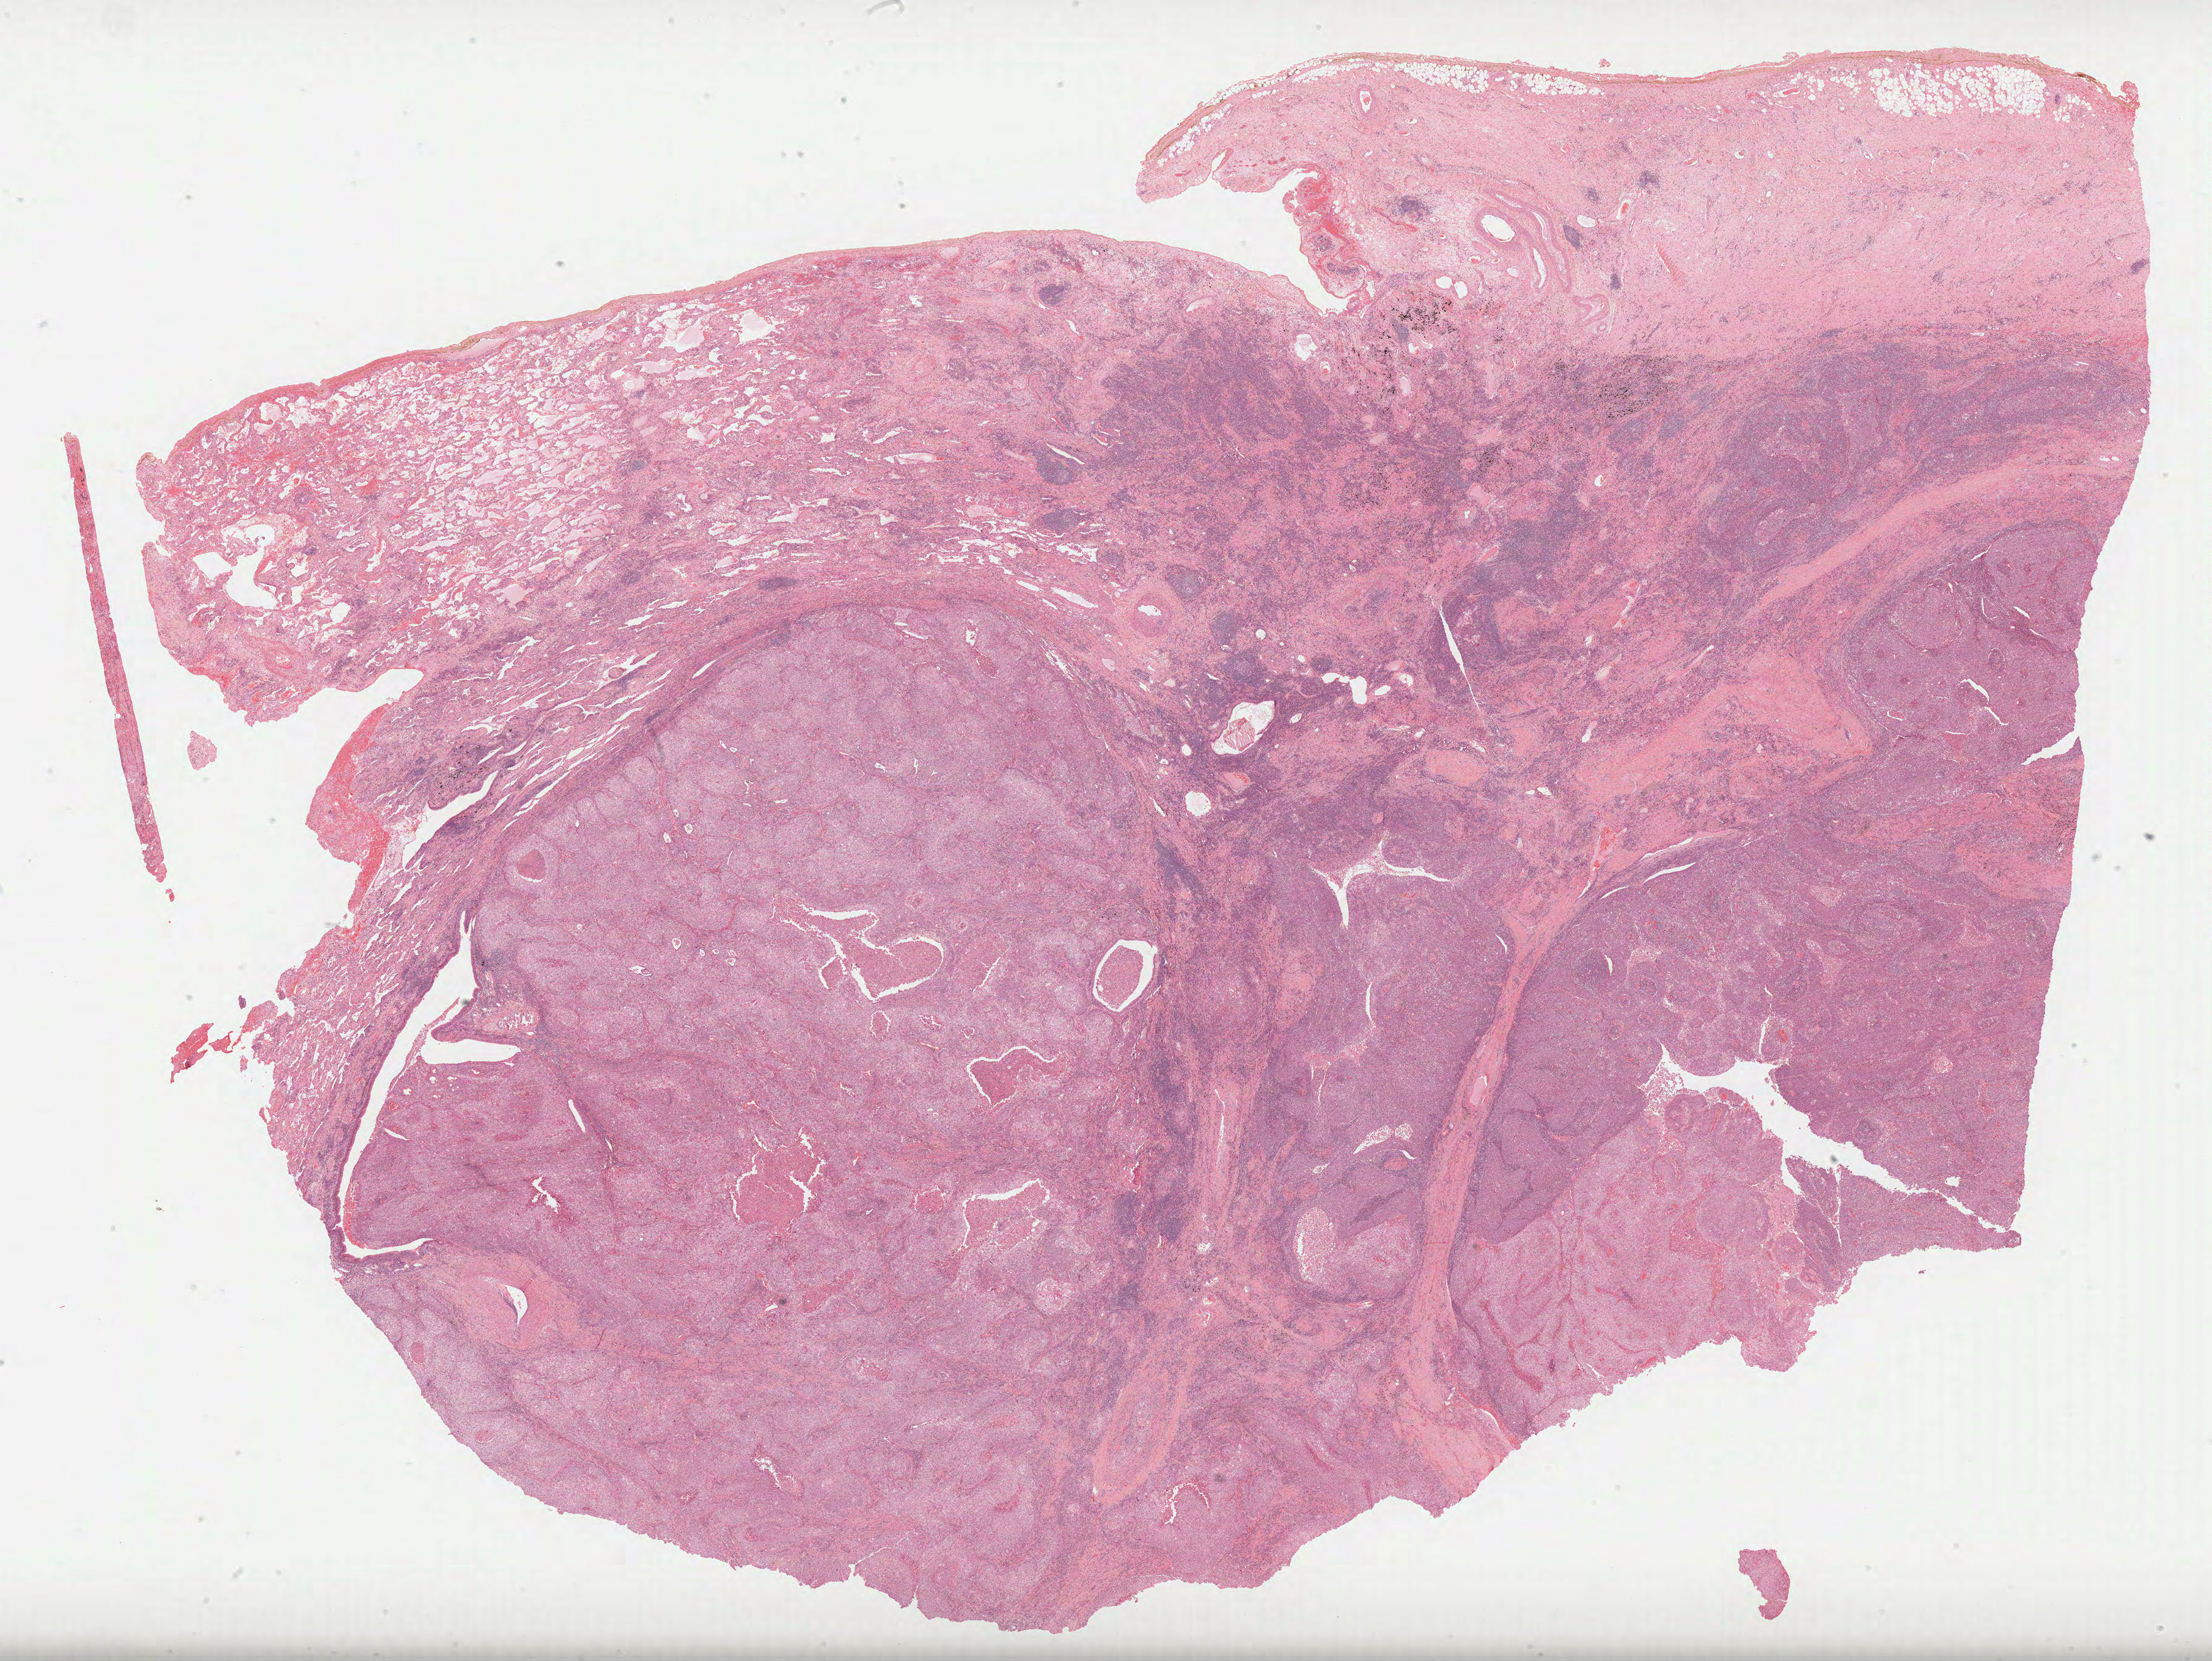
Digitized H&E-stained tissue section (whole slide) — whole scanned area (about 29.2 x 21.9 mm) shown as a low-resolution overview, formalin-fixed paraffin-embedded (FFPE) diagnostic section, sample: primary tumour, lung. Male, age 77 years at initial diagnosis.
• AJCC pathologic stage: IB
• histologic diagnosis: Squamous cell carcinoma, NOS (upper lobe, lung)